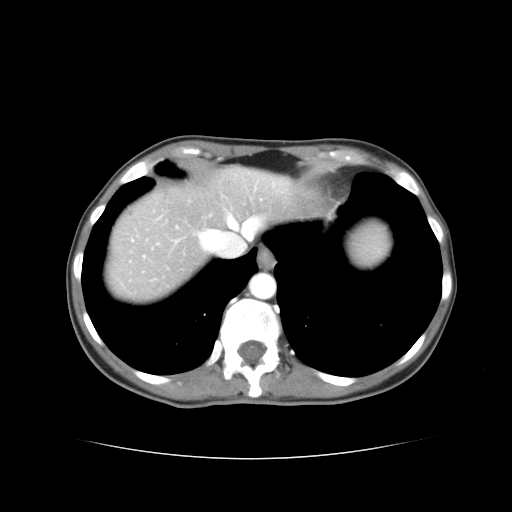
Contrast-enhanced abdominal CT, one axial slice; slice 34 of 38 in the series (ordered by position); 120 kVp; intravenous contrast given; soft-tissue window (W 400 / L 40 HU); 5 mm slice thickness; 512 × 512 image matrix, field of view 340 × 340 mm. Female patient, age 54 years. From the clinical record (not read from this slice): diagnosis: colorectal cancer liver metastases, imaged before liver resection; multiple liver metastases: yes; largest metastasis: 1.1 cm; disease in both lobes: yes.
Structures marked on this image (expert manual segmentation):
- hepatic veins: box from (x=202, y=217) to (x=261, y=246) px
- liver: (x=108, y=169)–(x=385, y=300)
- planned liver remnant (the part of the liver to remain after resection): (x=211, y=168)–(x=386, y=256)